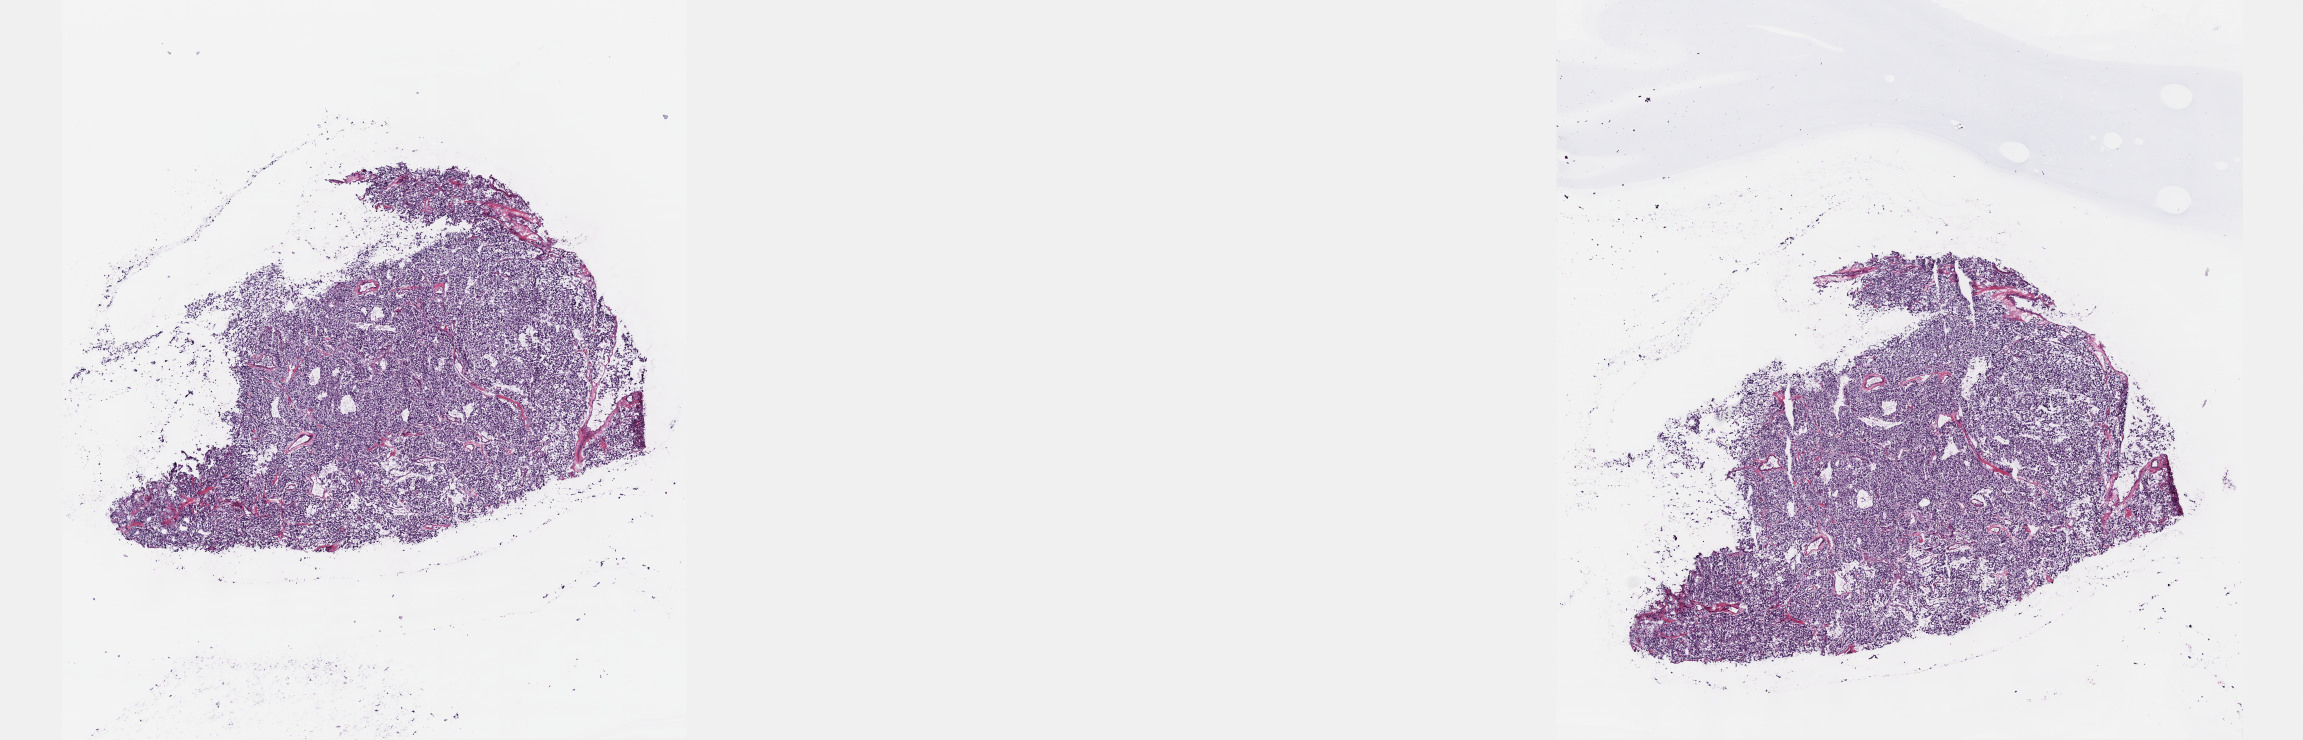
Whole-slide histology image, H&E, whole scanned area (about 18.6 x 6.0 mm, acquisition: 40x scan) shown as a low-resolution overview. Frozen section from the top of the tissue portion. Primary tumour sample from the adrenal gland. Female, age 30 years at initial diagnosis. Composition of this section per pathologist review: tumour cells 95%, tumour nuclei 95%, normal cells 0%, stromal cells 5%, necrosis 0%. Inflammatory infiltration, as recorded: lymphocyte infiltration 0%, monocyte infiltration 0%, neutrophil infiltration 0%.
* diagnosis: Pheochromocytoma, NOS